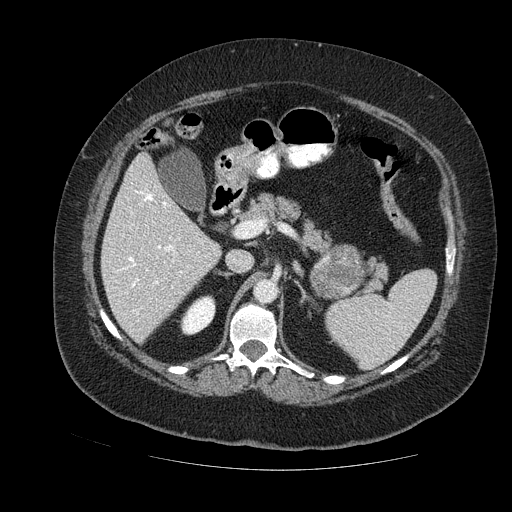
Contrast-enhanced abdominal CT, one axial slice. Slice 72 of 121 in the series (ordered by position). Soft-tissue window (W 400 / L 40 HU). 2.5 mm slice thickness. 512 × 512 image matrix, field of view 420 × 420 mm. Female patient. From the clinical record (not read from this slice): diagnosis: adrenocortical carcinoma; tumour side: left adrenal; tumour size at pathology: 8 cm; Ki-67 index: 7 %.
Annotated regions visible in this slice (semi-automatic segmentation, software-assisted and operator-edited):
- mass: bounding box (x1, y1, x2, y2) in pixels: (311, 243, 367, 299)